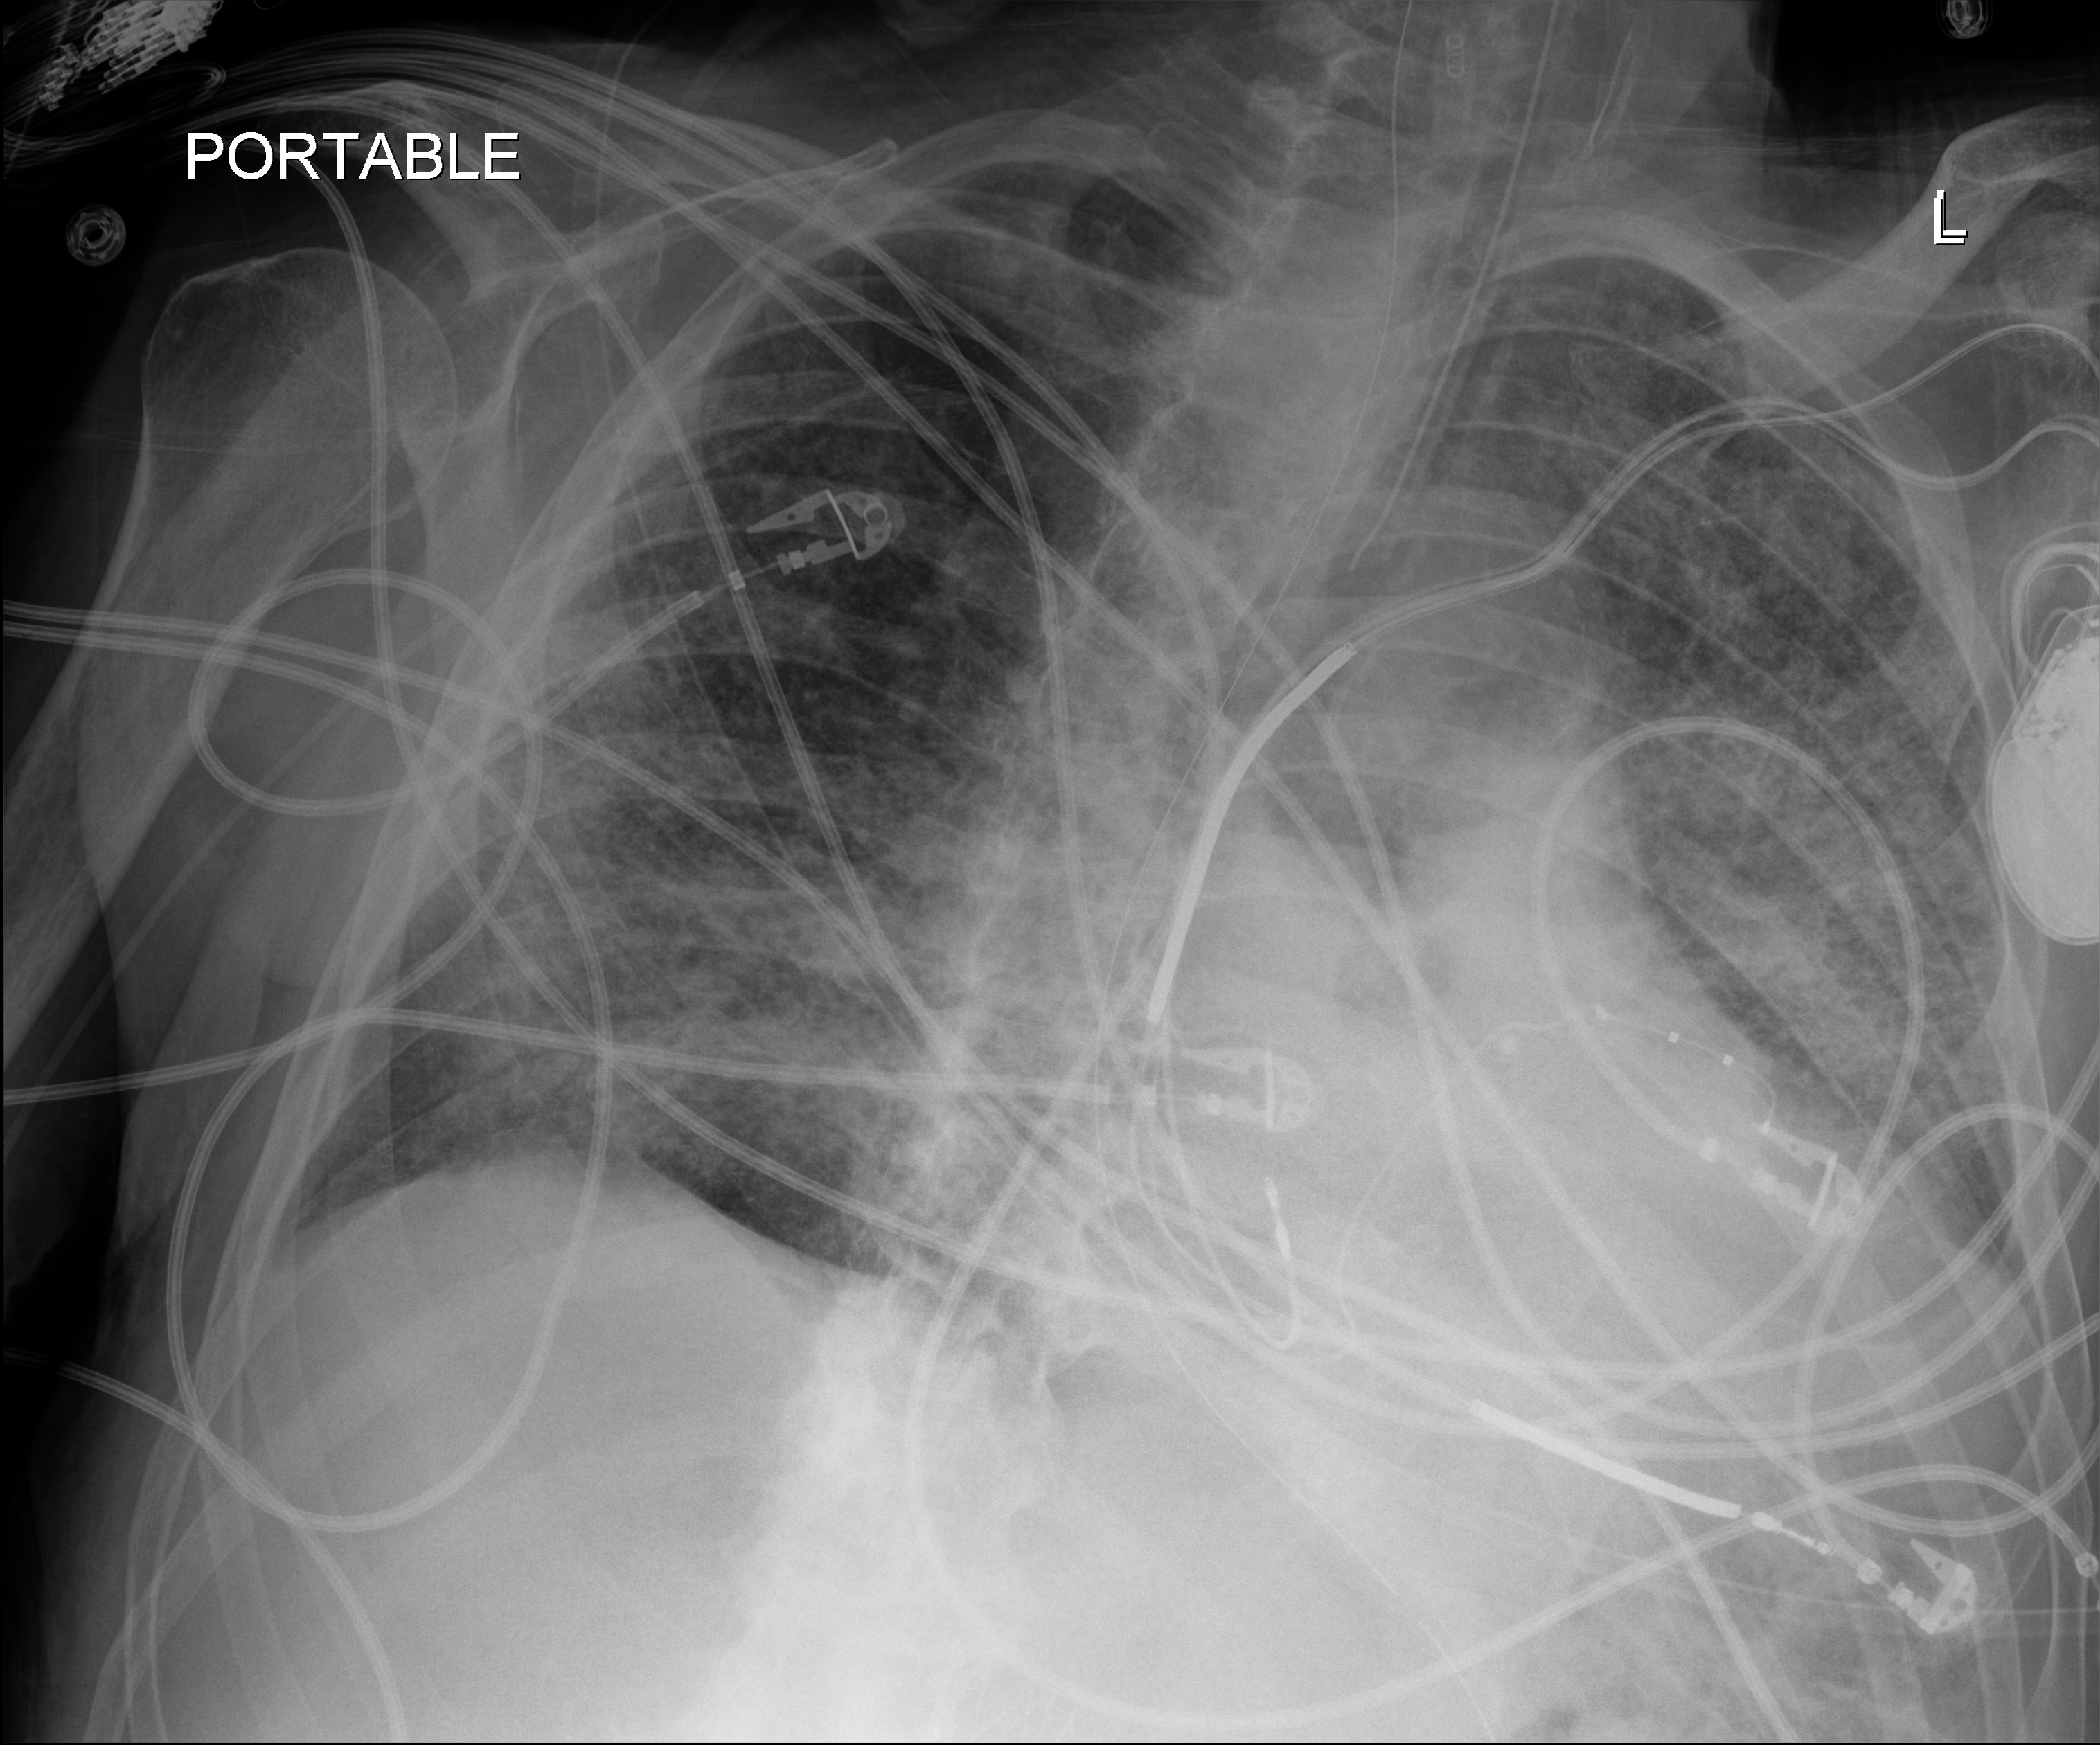
Bedside chest radiograph (digital radiography), anteroposterior (AP) projection. Male patient hospitalised with COVID-19, age 60–74 years.
Admission-level facts for this patient (not findings on this image; timing relative to this image not recorded): mechanically ventilated during this hospital stay: yes.